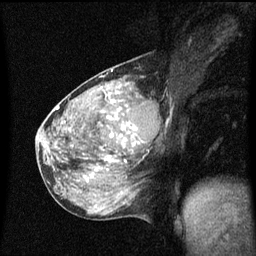
Breast MRI (dynamic contrast-enhanced), one sagittal slice; dynamic contrast-enhanced series, image 2 of 3 at this slice position (ordered by acquisition); 1.5 T; TE 4.2 ms, TR 8.4 ms; 2 mm slice thickness; 256 × 256 image matrix, field of view 200 × 200 mm. Female patient, age 49 years.
Annotated regions visible in this slice (semi-automatic segmentation, software-assisted and operator-edited):
- analysis volume of interest (the breast-tissue region the enhancement analysis was run in; not a lesion): bounding box <103,90,157,151> (left, top, right, bottom; pixels)
- tumour enhancement mask (voxels above the 70 % enhancement threshold inside the analysis volume of interest): <106,92,134,141>